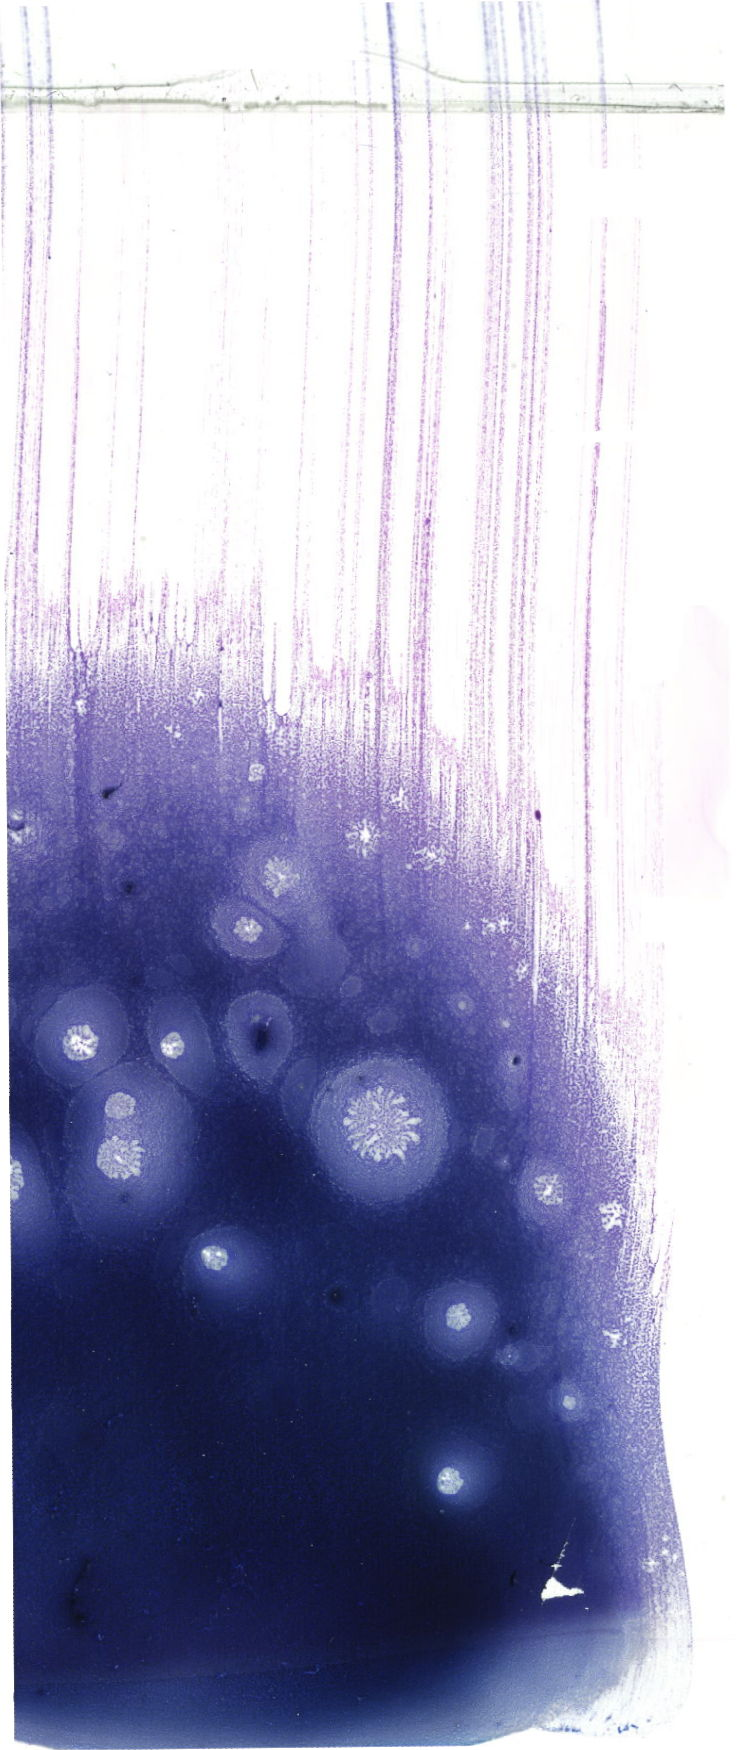
Whole-slide image of a May-Grünwald–Giemsa-stained bone marrow aspirate smear, whole scanned area (about 20.9 x 49.6 mm) shown as a low-resolution overview. Male patient.
Diagnosis: B Acute Lymphoblastic Leukemia.